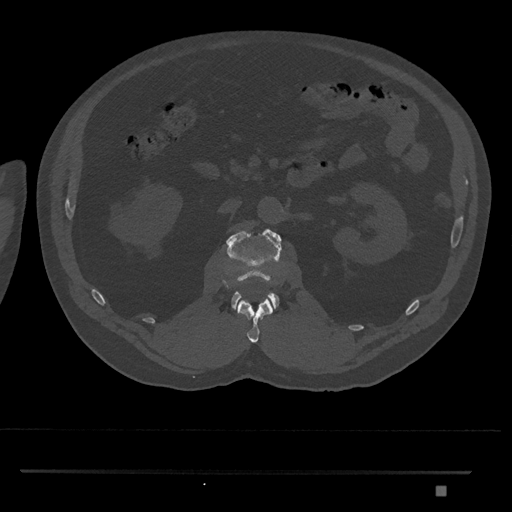
CT including the spine, one axial slice; position 789 of 1134 along the scan axis; reconstruction kernel Br40s/3; 120 kVp; bone window (W 1800 / L 400 HU); 512 × 512 image matrix, field of view 429 × 429 mm. Male patient, age 65 years. Case-level facts recorded for this patient, not image findings: primary cancer: prostate.
Outlined on this slice (semi-automatically segmented with operator editing):
- L1 vertebra: bounding box [x1, y1, x2, y2] px = [237, 298, 273, 343]
- L2 vertebra: [226, 228, 282, 310]